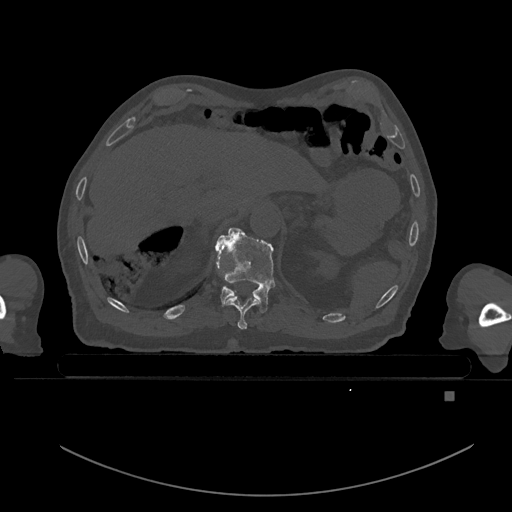
CT including the spine, one axial slice. Bone window (W 1800 / L 400 HU). 512 × 512 image matrix. Male patient, age 82 years. Case-level facts recorded for this patient, not image findings: primary cancer: prostate; vertebrae with lytic lesions (as recorded): T11, T9, T8, T2.
Annotated regions visible in this slice (semi-automatically segmented with operator editing):
- T10 vertebra: bounding box [x1, y1, x2, y2] px = [225, 296, 259, 330]
- T11 vertebra: [216, 227, 275, 313]